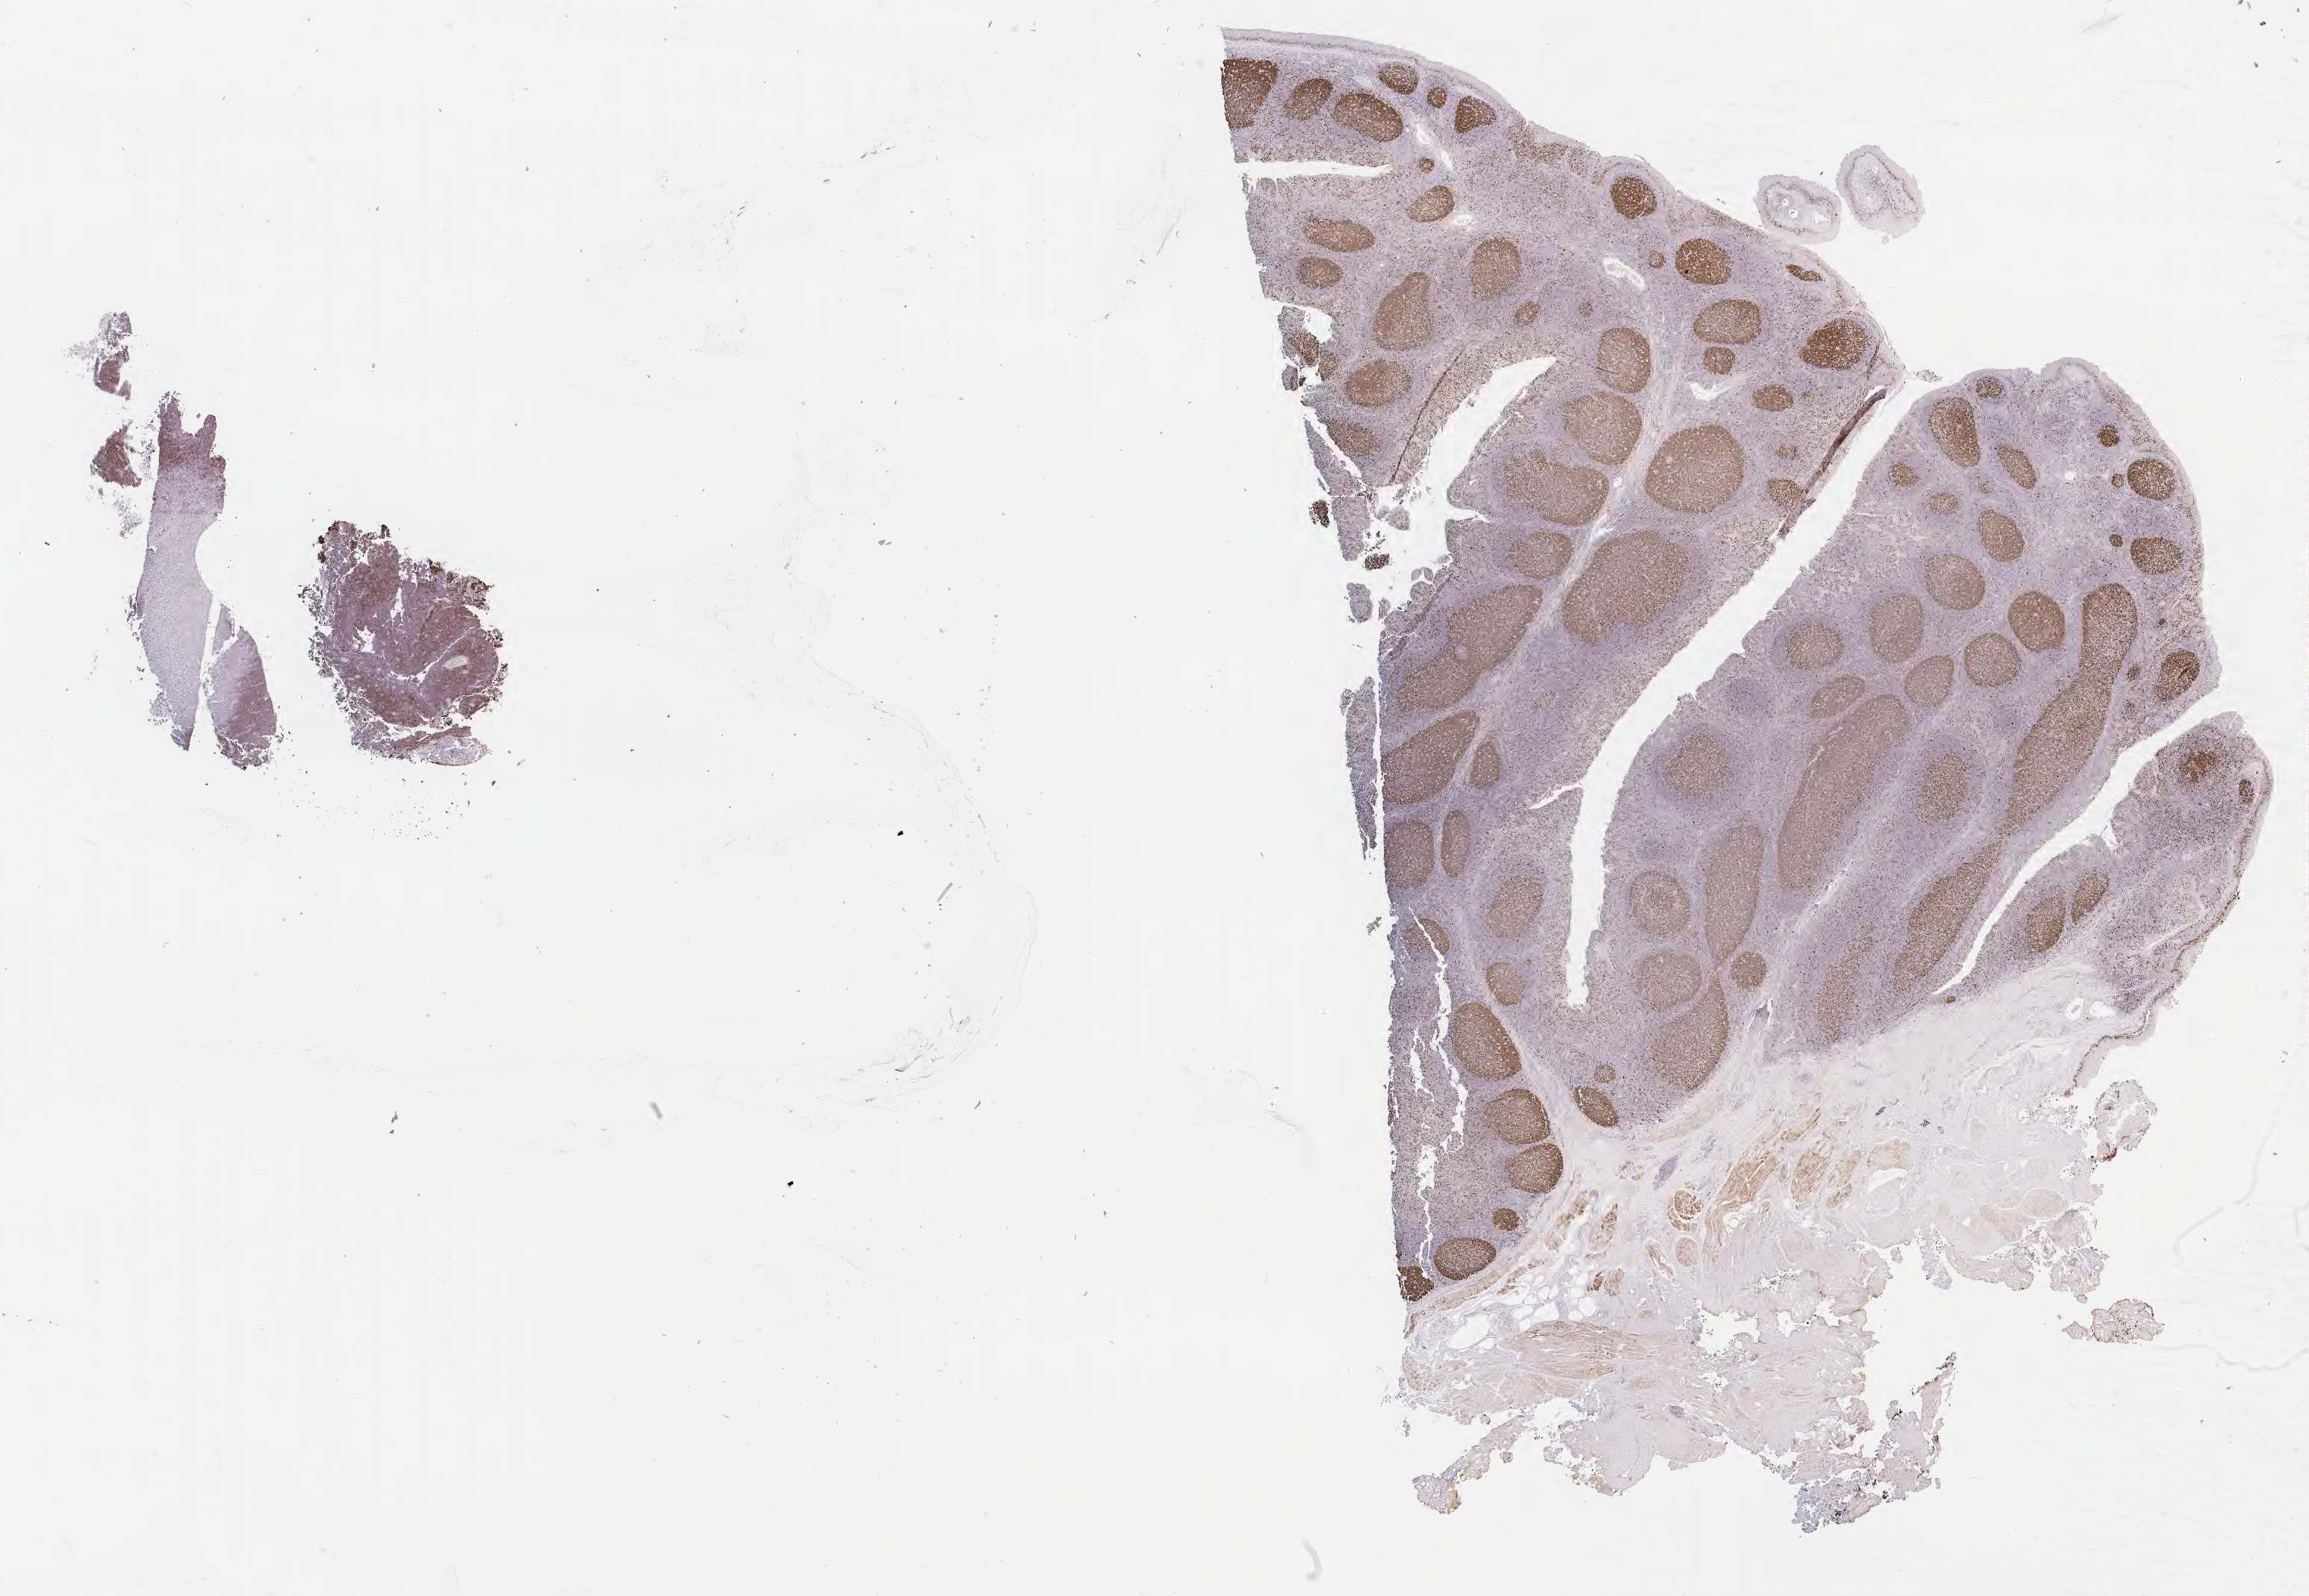
Whole-slide image, immunohistochemical stain for Ki-67 — a low-resolution overview of the entire scanned area, about 24.7 x 17.0 mm, tumor tissue, anatomic site: cranium. Male, age 4 years at initial diagnosis.
- diagnosis: Burkitt lymphoma, NOS